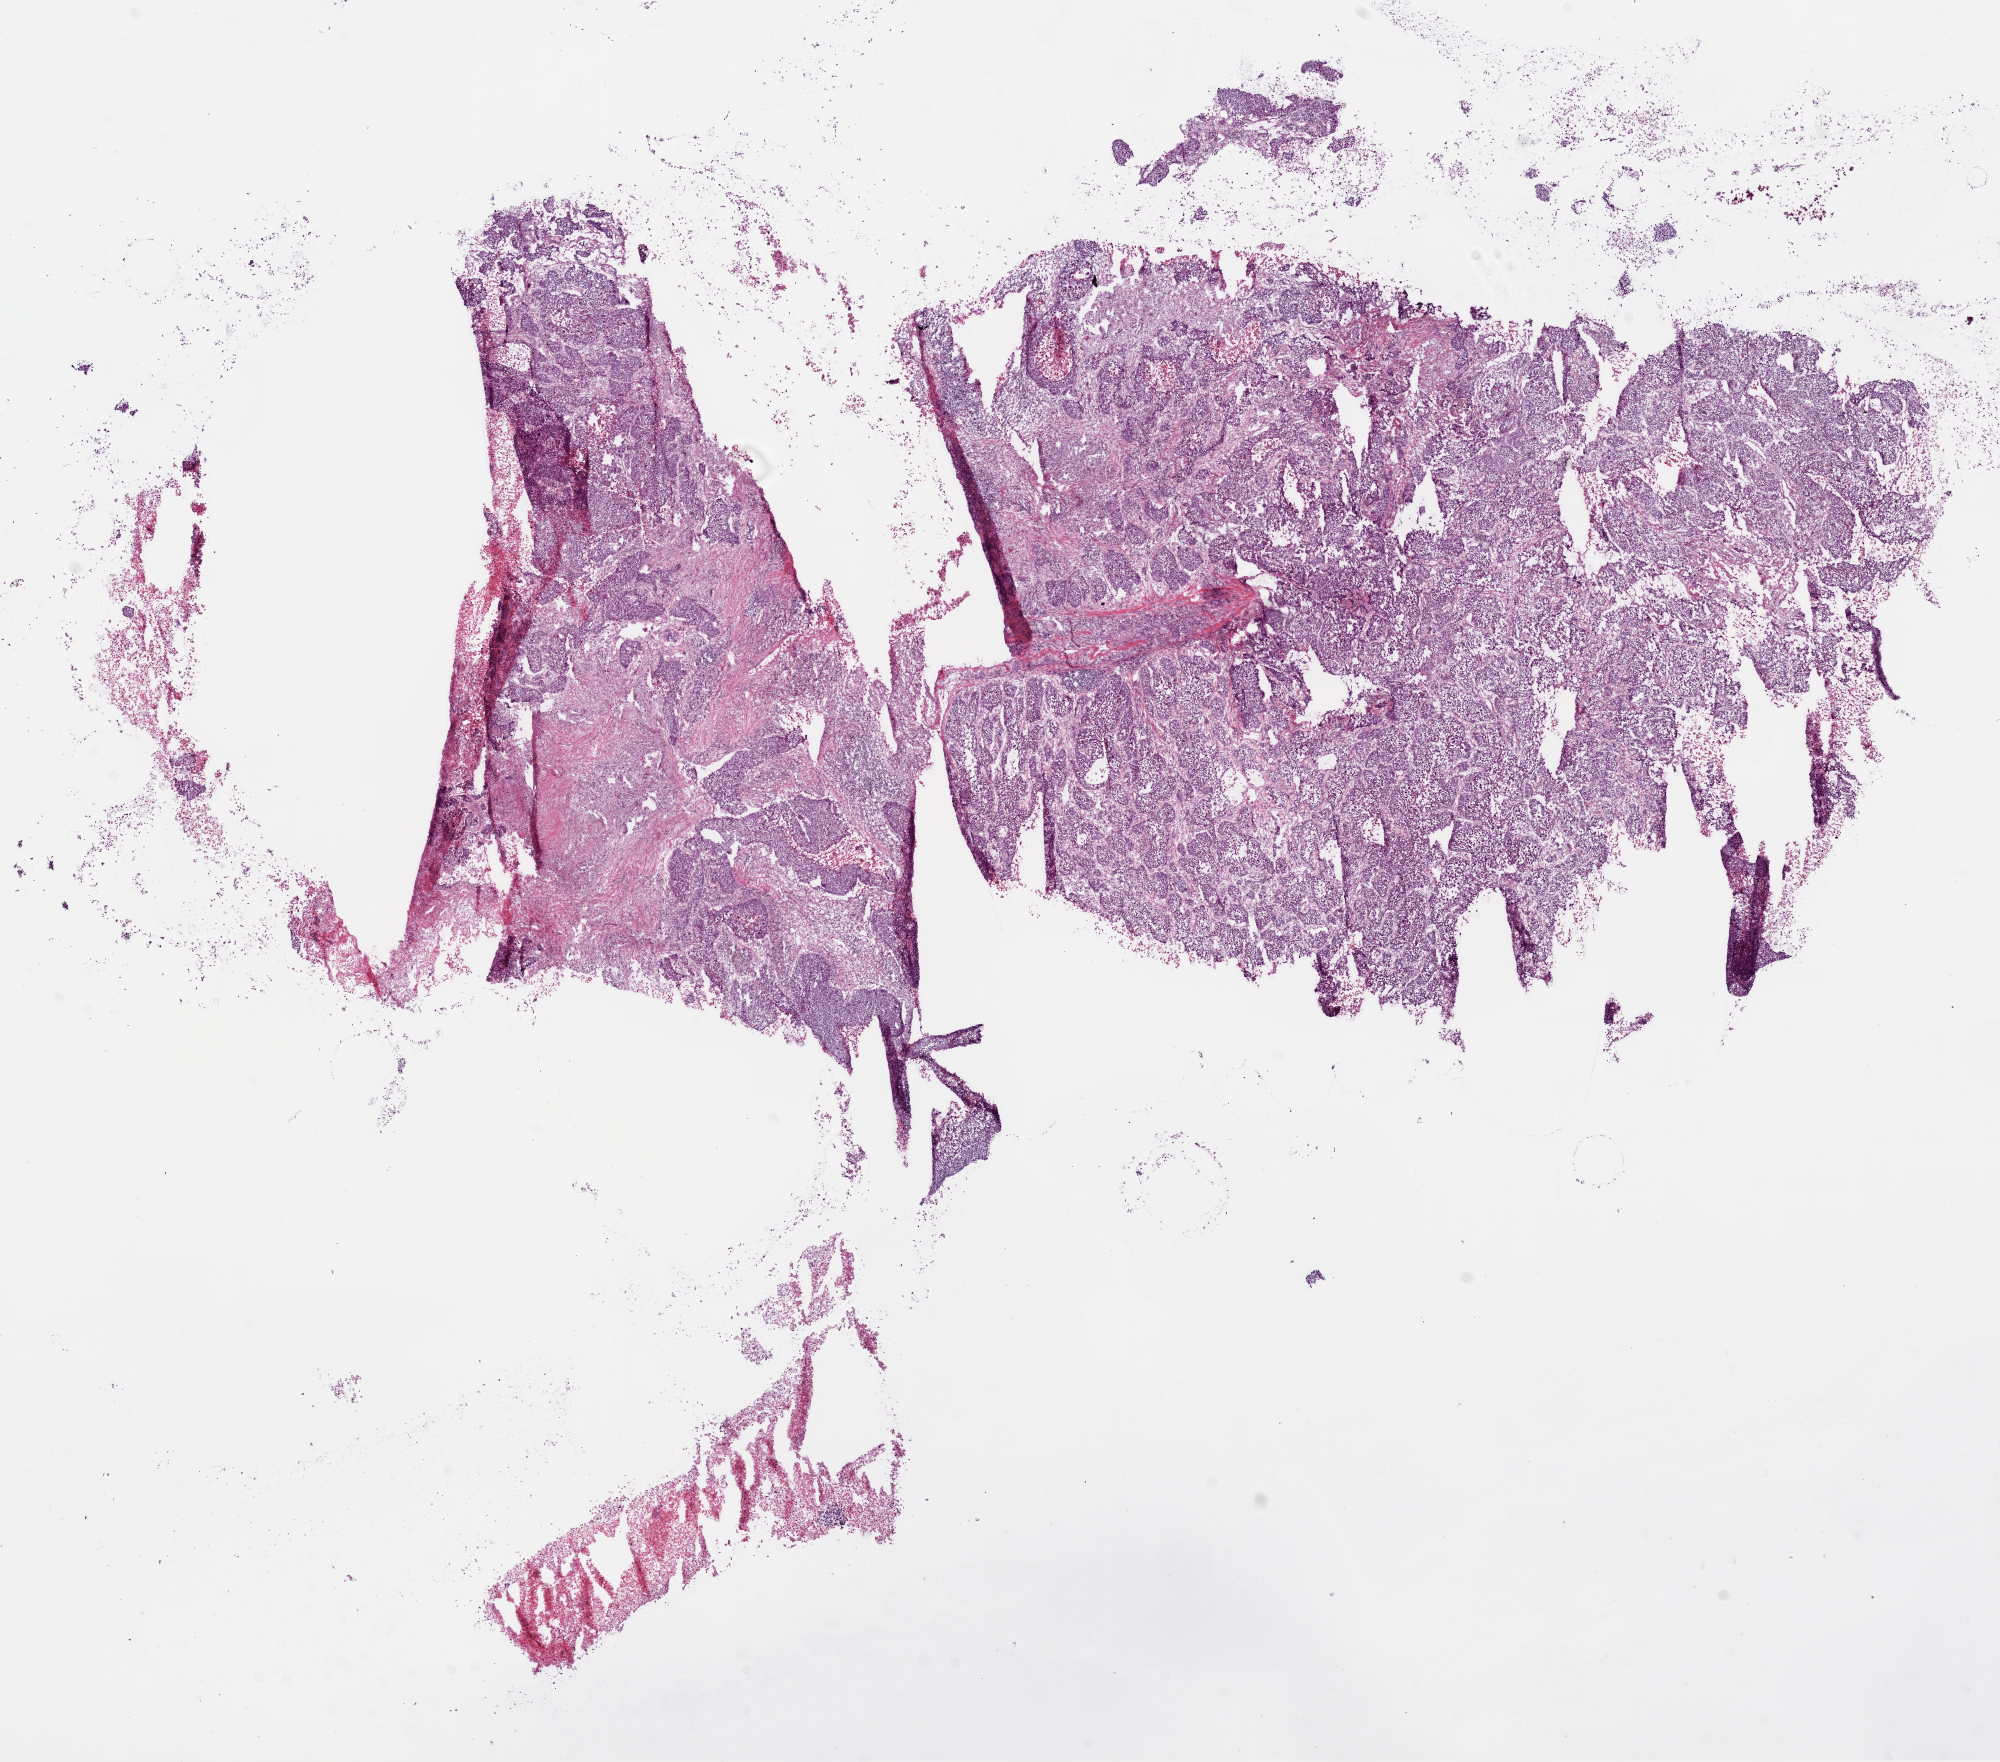
Digitized H&E tissue section (whole slide) — low-resolution overview of the scanned area, about 16.0 x 14.1 mm, frozen section from the bottom of the tissue portion, sample: primary tumour, lung. Female patient; age at initial diagnosis 73 years. Slide review estimates, as recorded: tumour cells 75%, tumour nuclei 80%, normal cells 0%, stromal cells 15%, necrosis 10%.
Laterality: left. AJCC pathologic stage: IIB (6th edition). Pathologic diagnosis: Basaloid squamous cell carcinoma (upper lobe, lung).